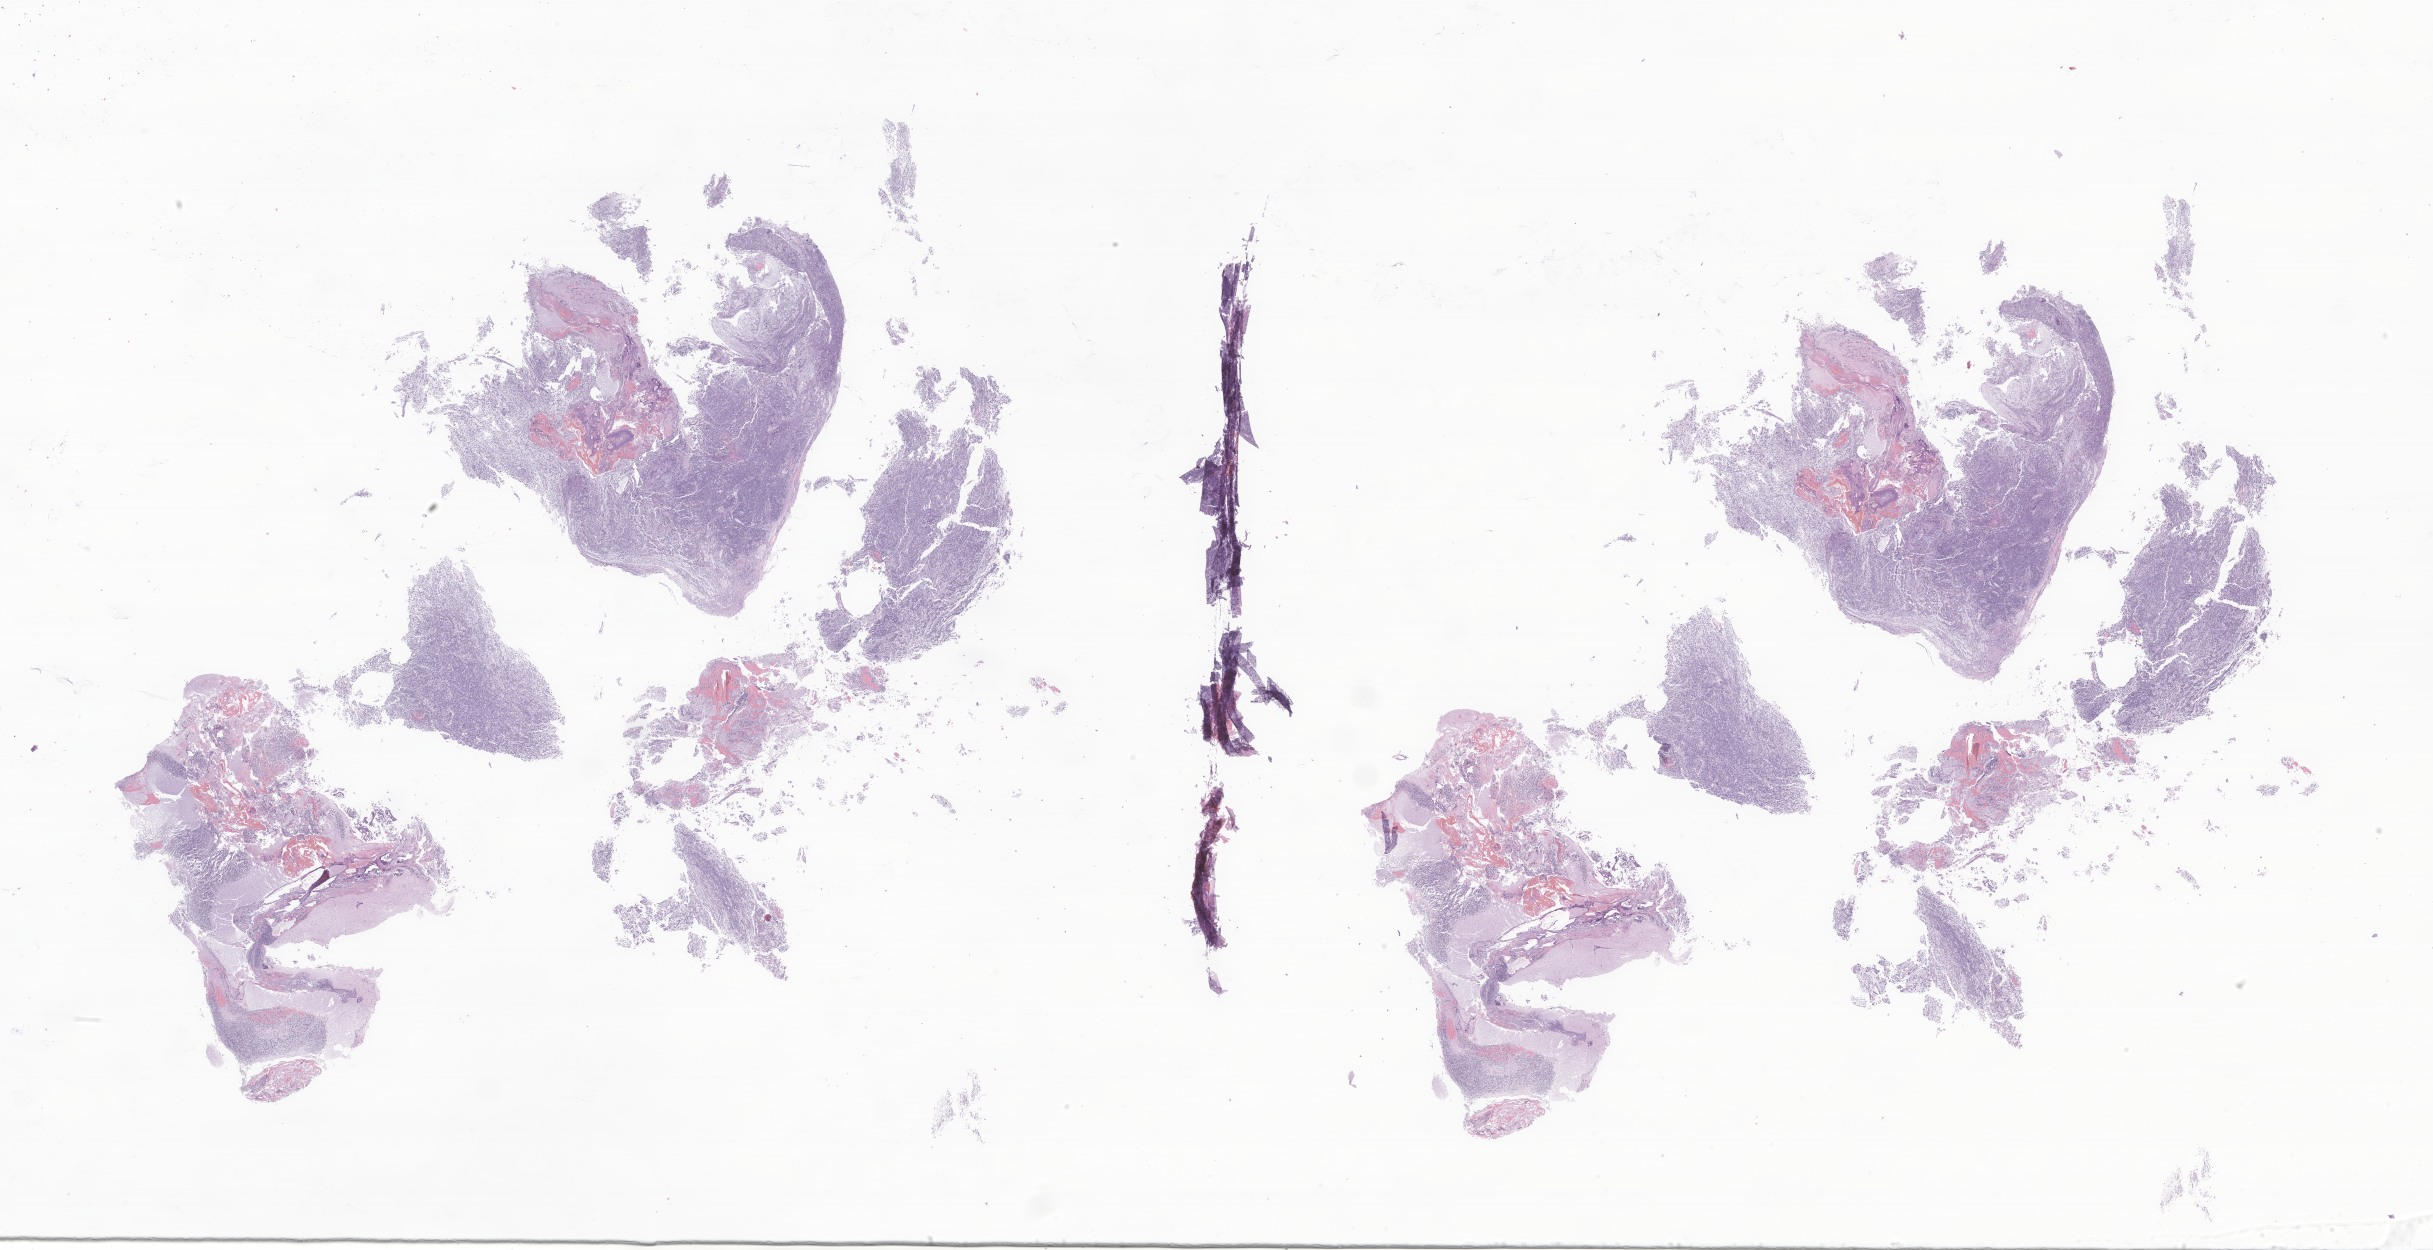
H&E whole-slide image of tumor tissue from the brain — whole scanned area (about 41.0 x 21.1 mm) shown as a low-resolution overview, FFPE section. Patient: female, age 565 days.
• diagnosis: Neoplasm, malignant